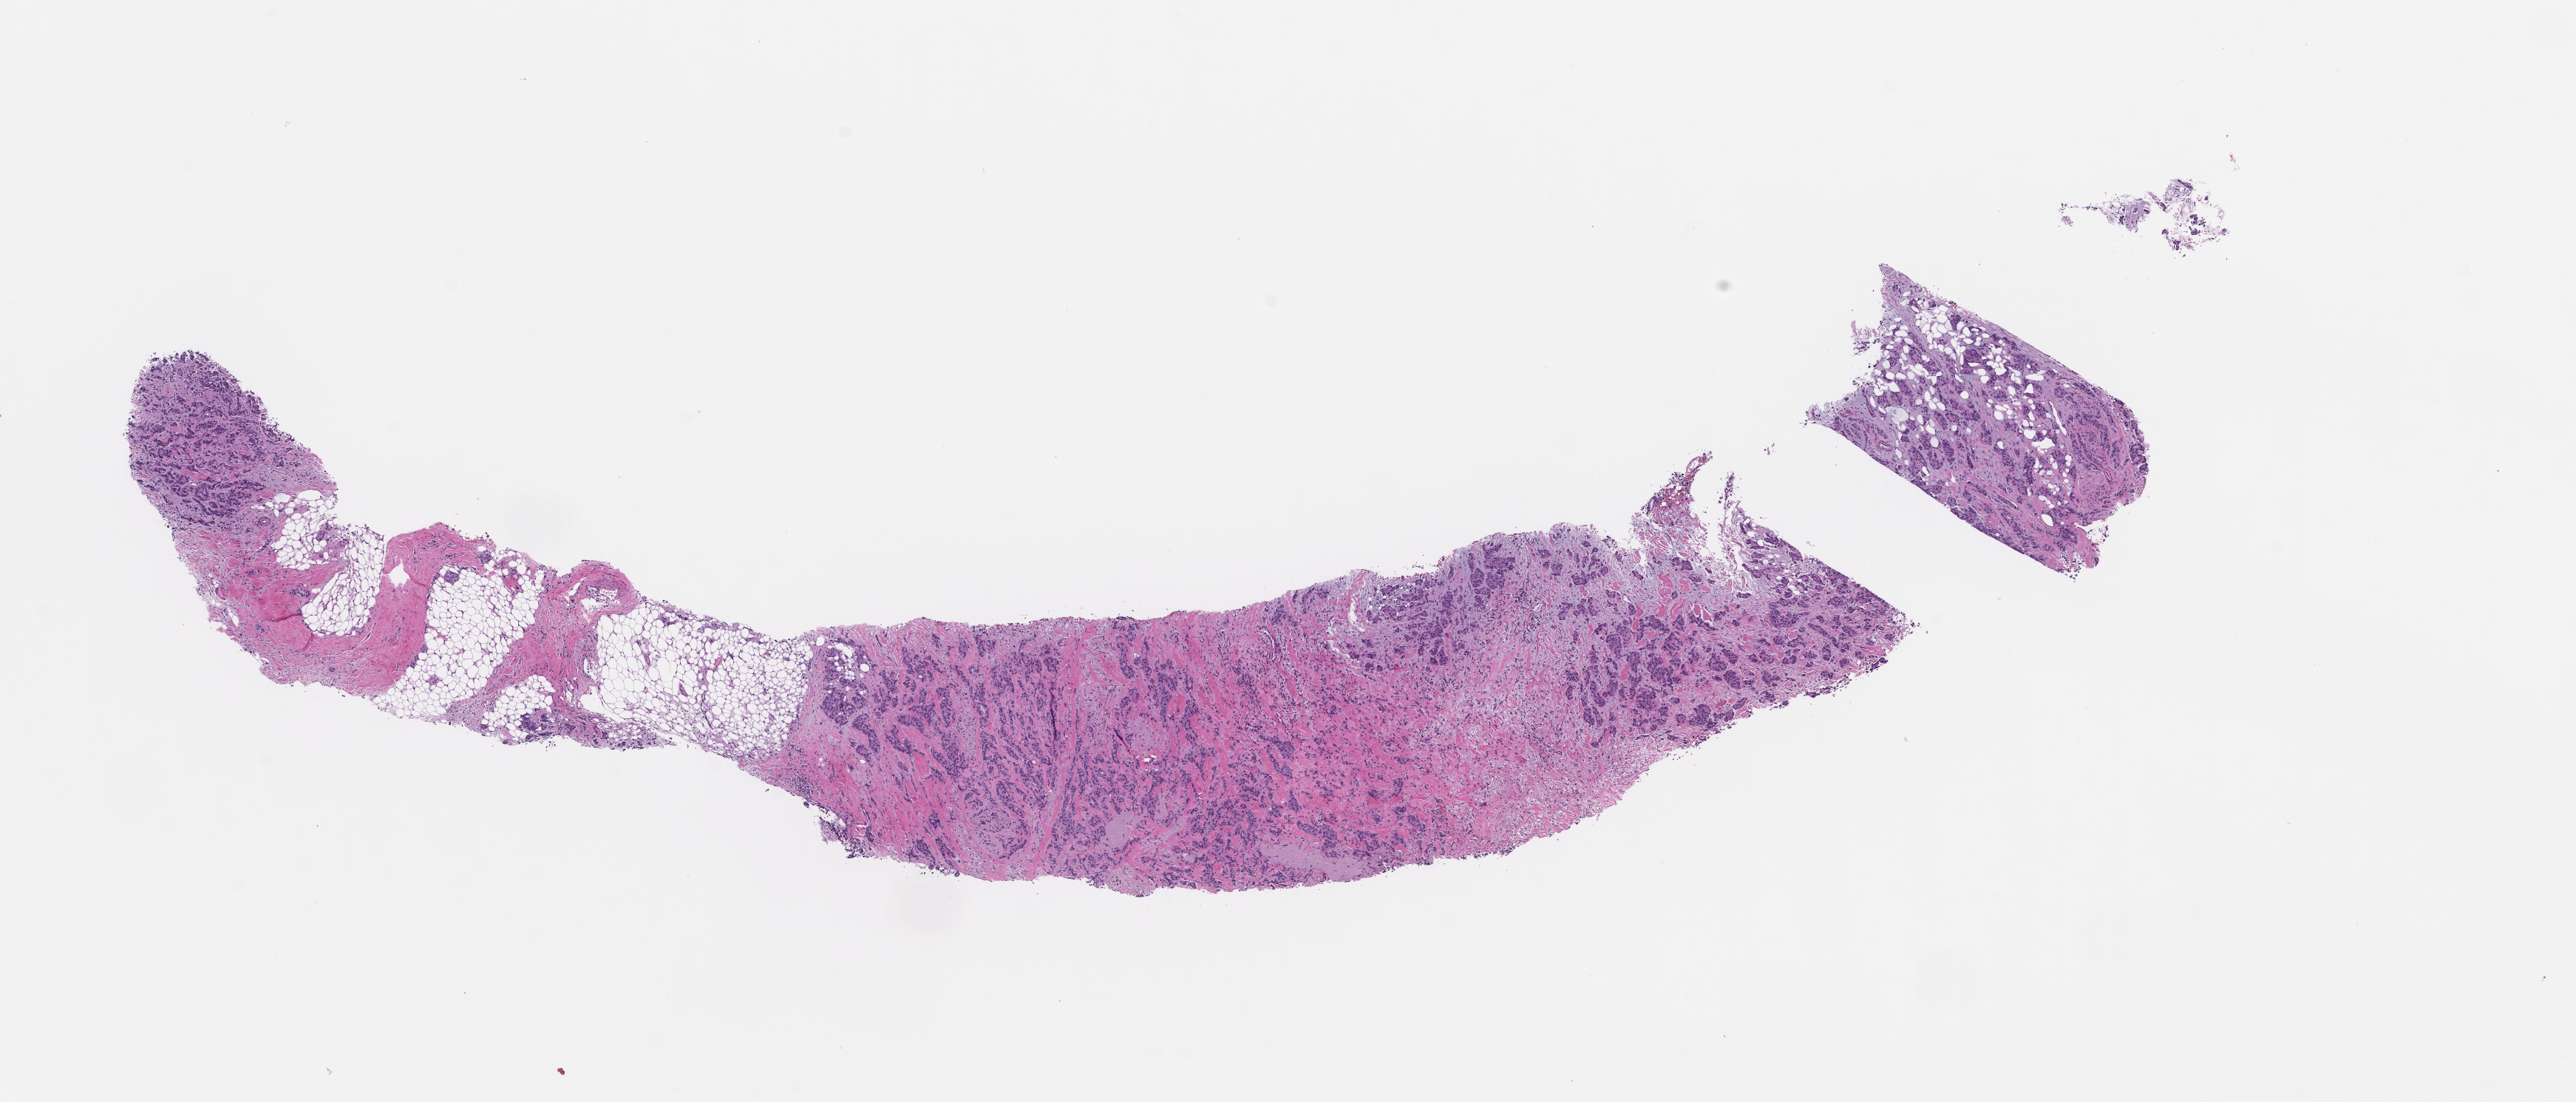
Digitized H&E-stained section, a low-resolution overview of the entire scanned area, about 14.1 x 6.0 mm; formalin-fixed, paraffin-embedded (FFPE) tissue; site: breast. Female patient.
- this section: primary tumor
- diagnosis: Invasive Breast Carcinoma